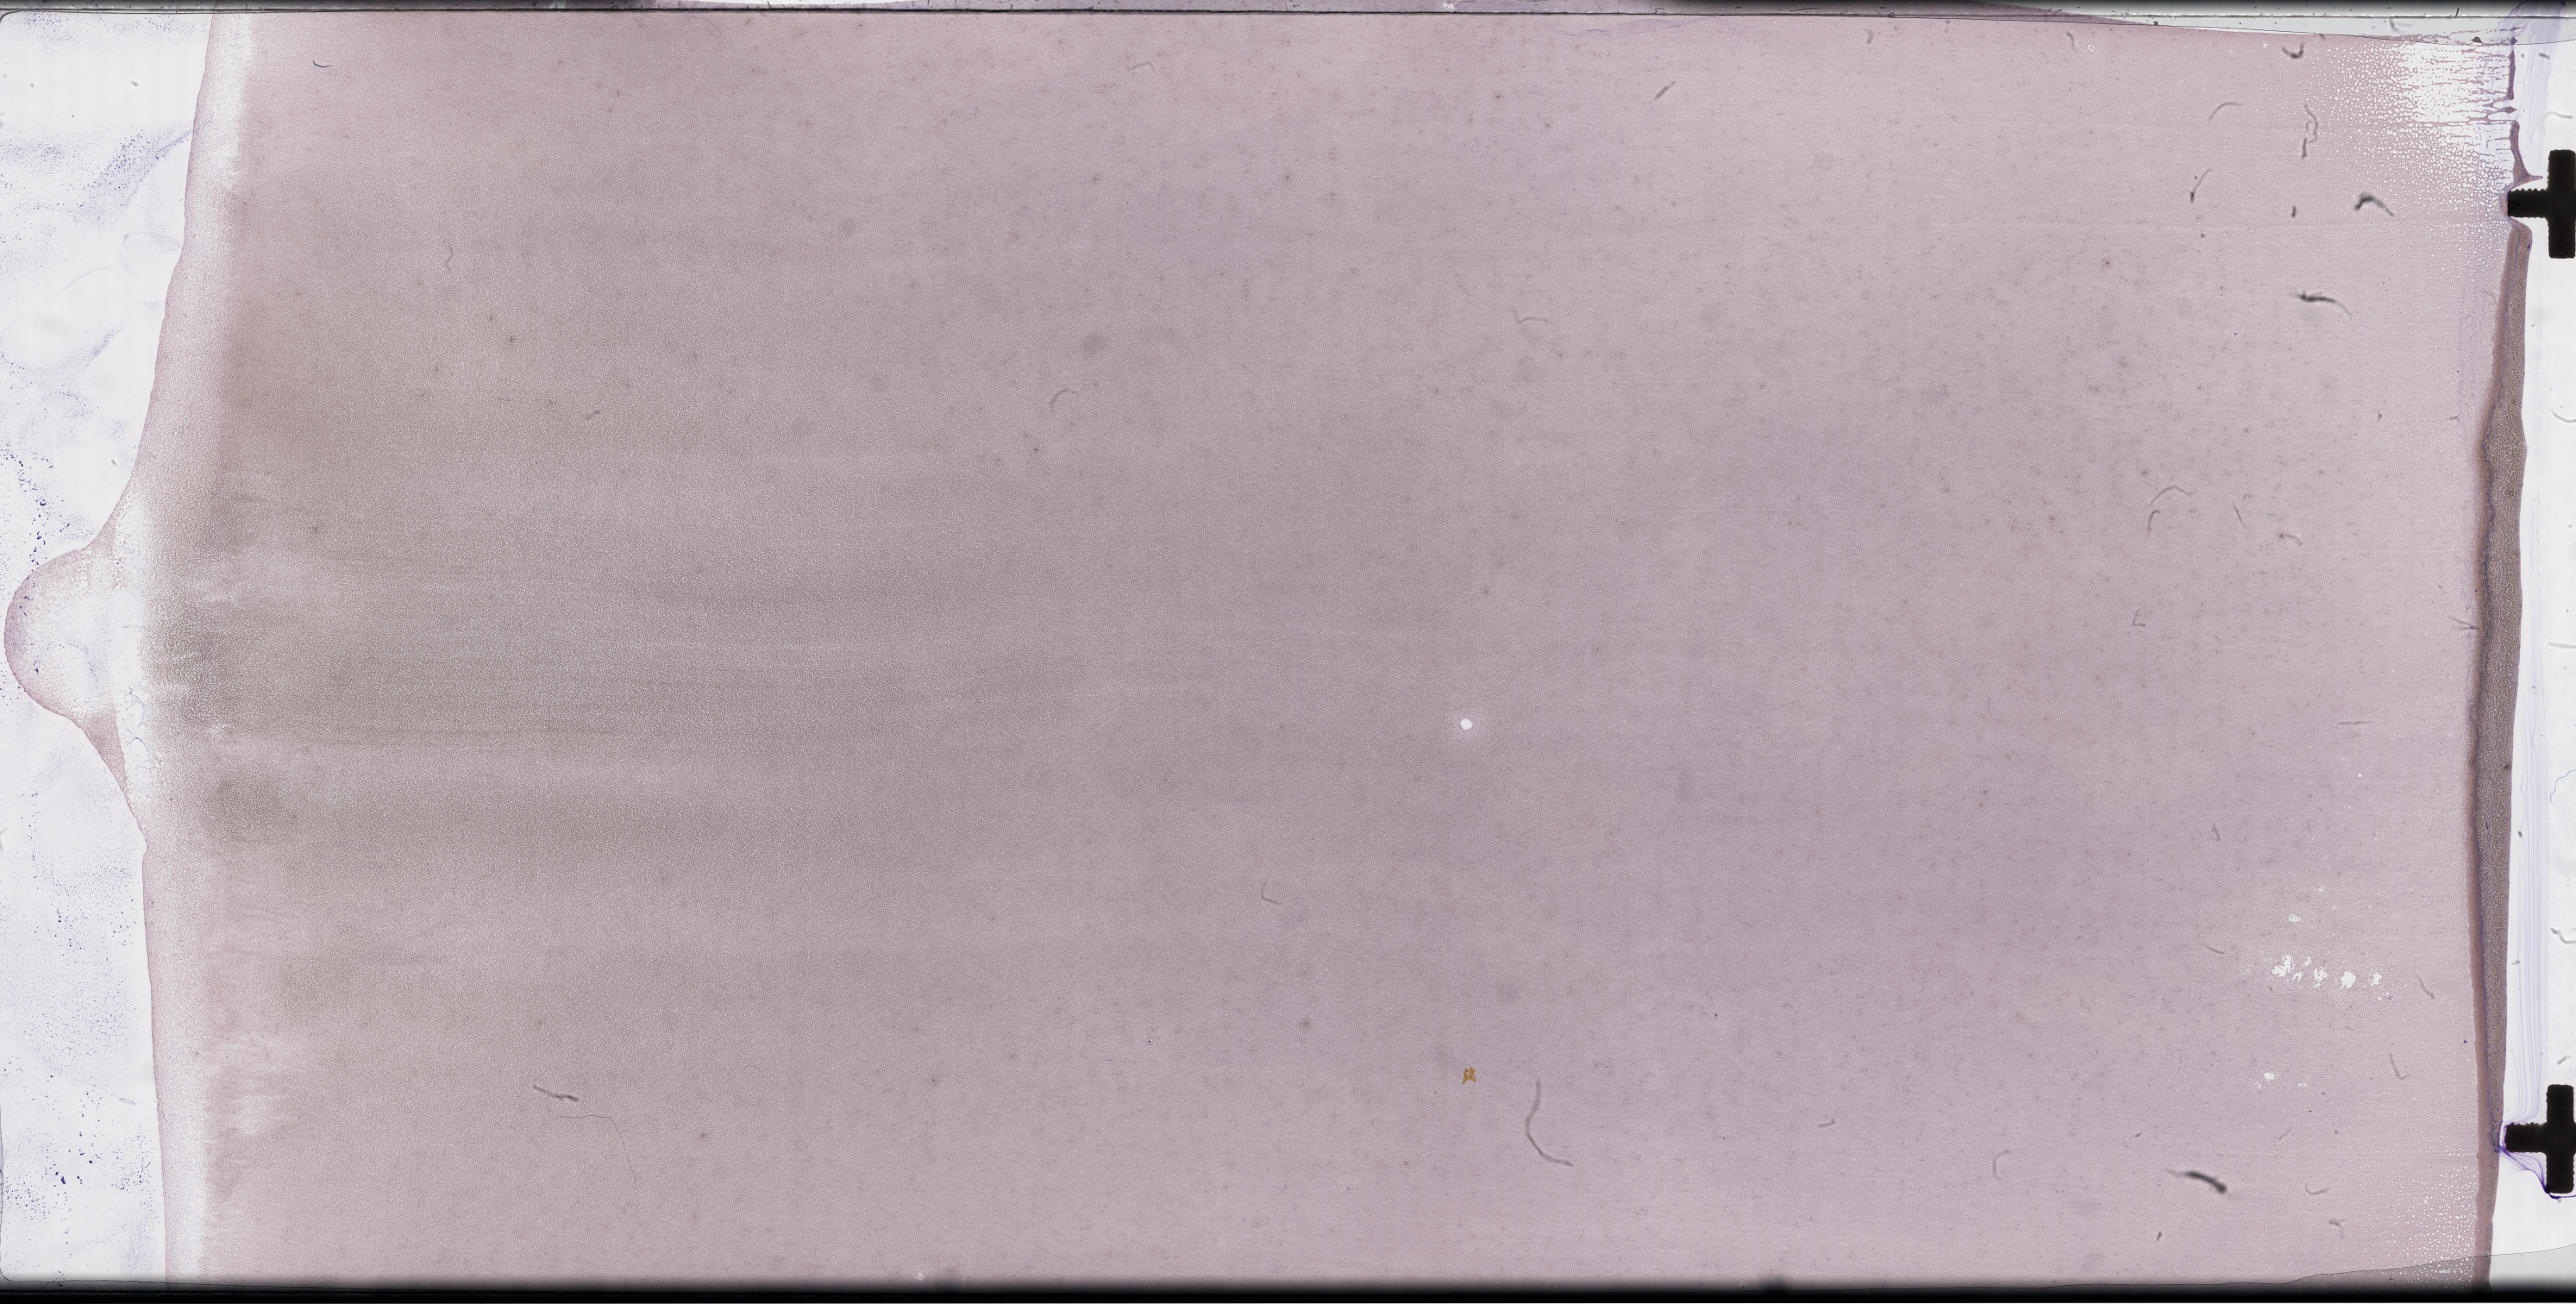
Whole-slide image of a whole blood smear, Wright-Giemsa stain, low-resolution overview of the scanned area, about 48.2 x 24.4 mm. Smear from an EDTA sample. Collected on treatment. Male patient.
From a patient with: Plasma Cell Myeloma.